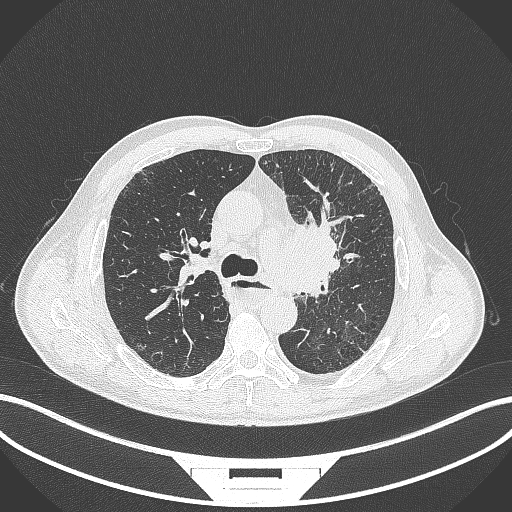
Chest CT, one axial slice. Slice 253 of 411 in the series (ordered by position). 120 kVp. Lung window (W 1500 / L -600 HU). 1 mm slice thickness. 512 × 512 image matrix, field of view 400 × 400 mm. Male patient, age 57 years. From the clinical record (not read from this slice): clinical TNM (as recorded): T2a N1 M0.
Outlined on this slice (rectangle marked by the reading radiologist):
- lung tumour (recorded histology: squamous cell carcinoma): bounding box [x1, y1, x2, y2] px = [276, 211, 346, 311]